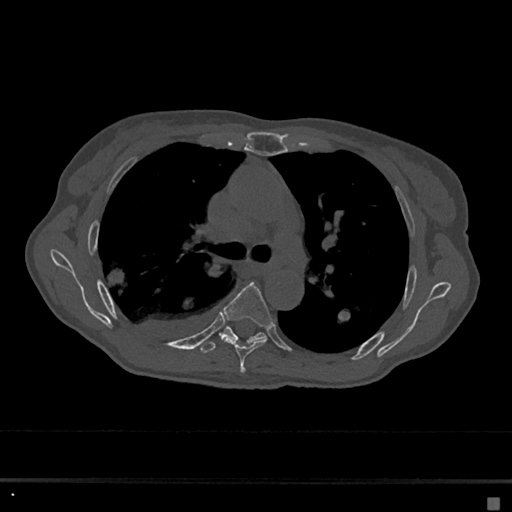
CT including the spine, one axial slice; position 447 of 797 along the scan axis; reconstruction kernel Br40s/3; 120 kVp; bone window (W 1800 / L 400 HU); 512 × 512 image matrix, field of view 360 × 360 mm. Female patient, age 68 years. Case-level facts recorded for this patient, not image findings: primary cancer: renal.
Structures marked on this image (semi-automatic segmentation, software-assisted and operator-edited):
- T5 vertebra: bounding box [x1, y1, x2, y2] px = [224, 282, 272, 373]
- T6 vertebra: [200, 327, 266, 353]